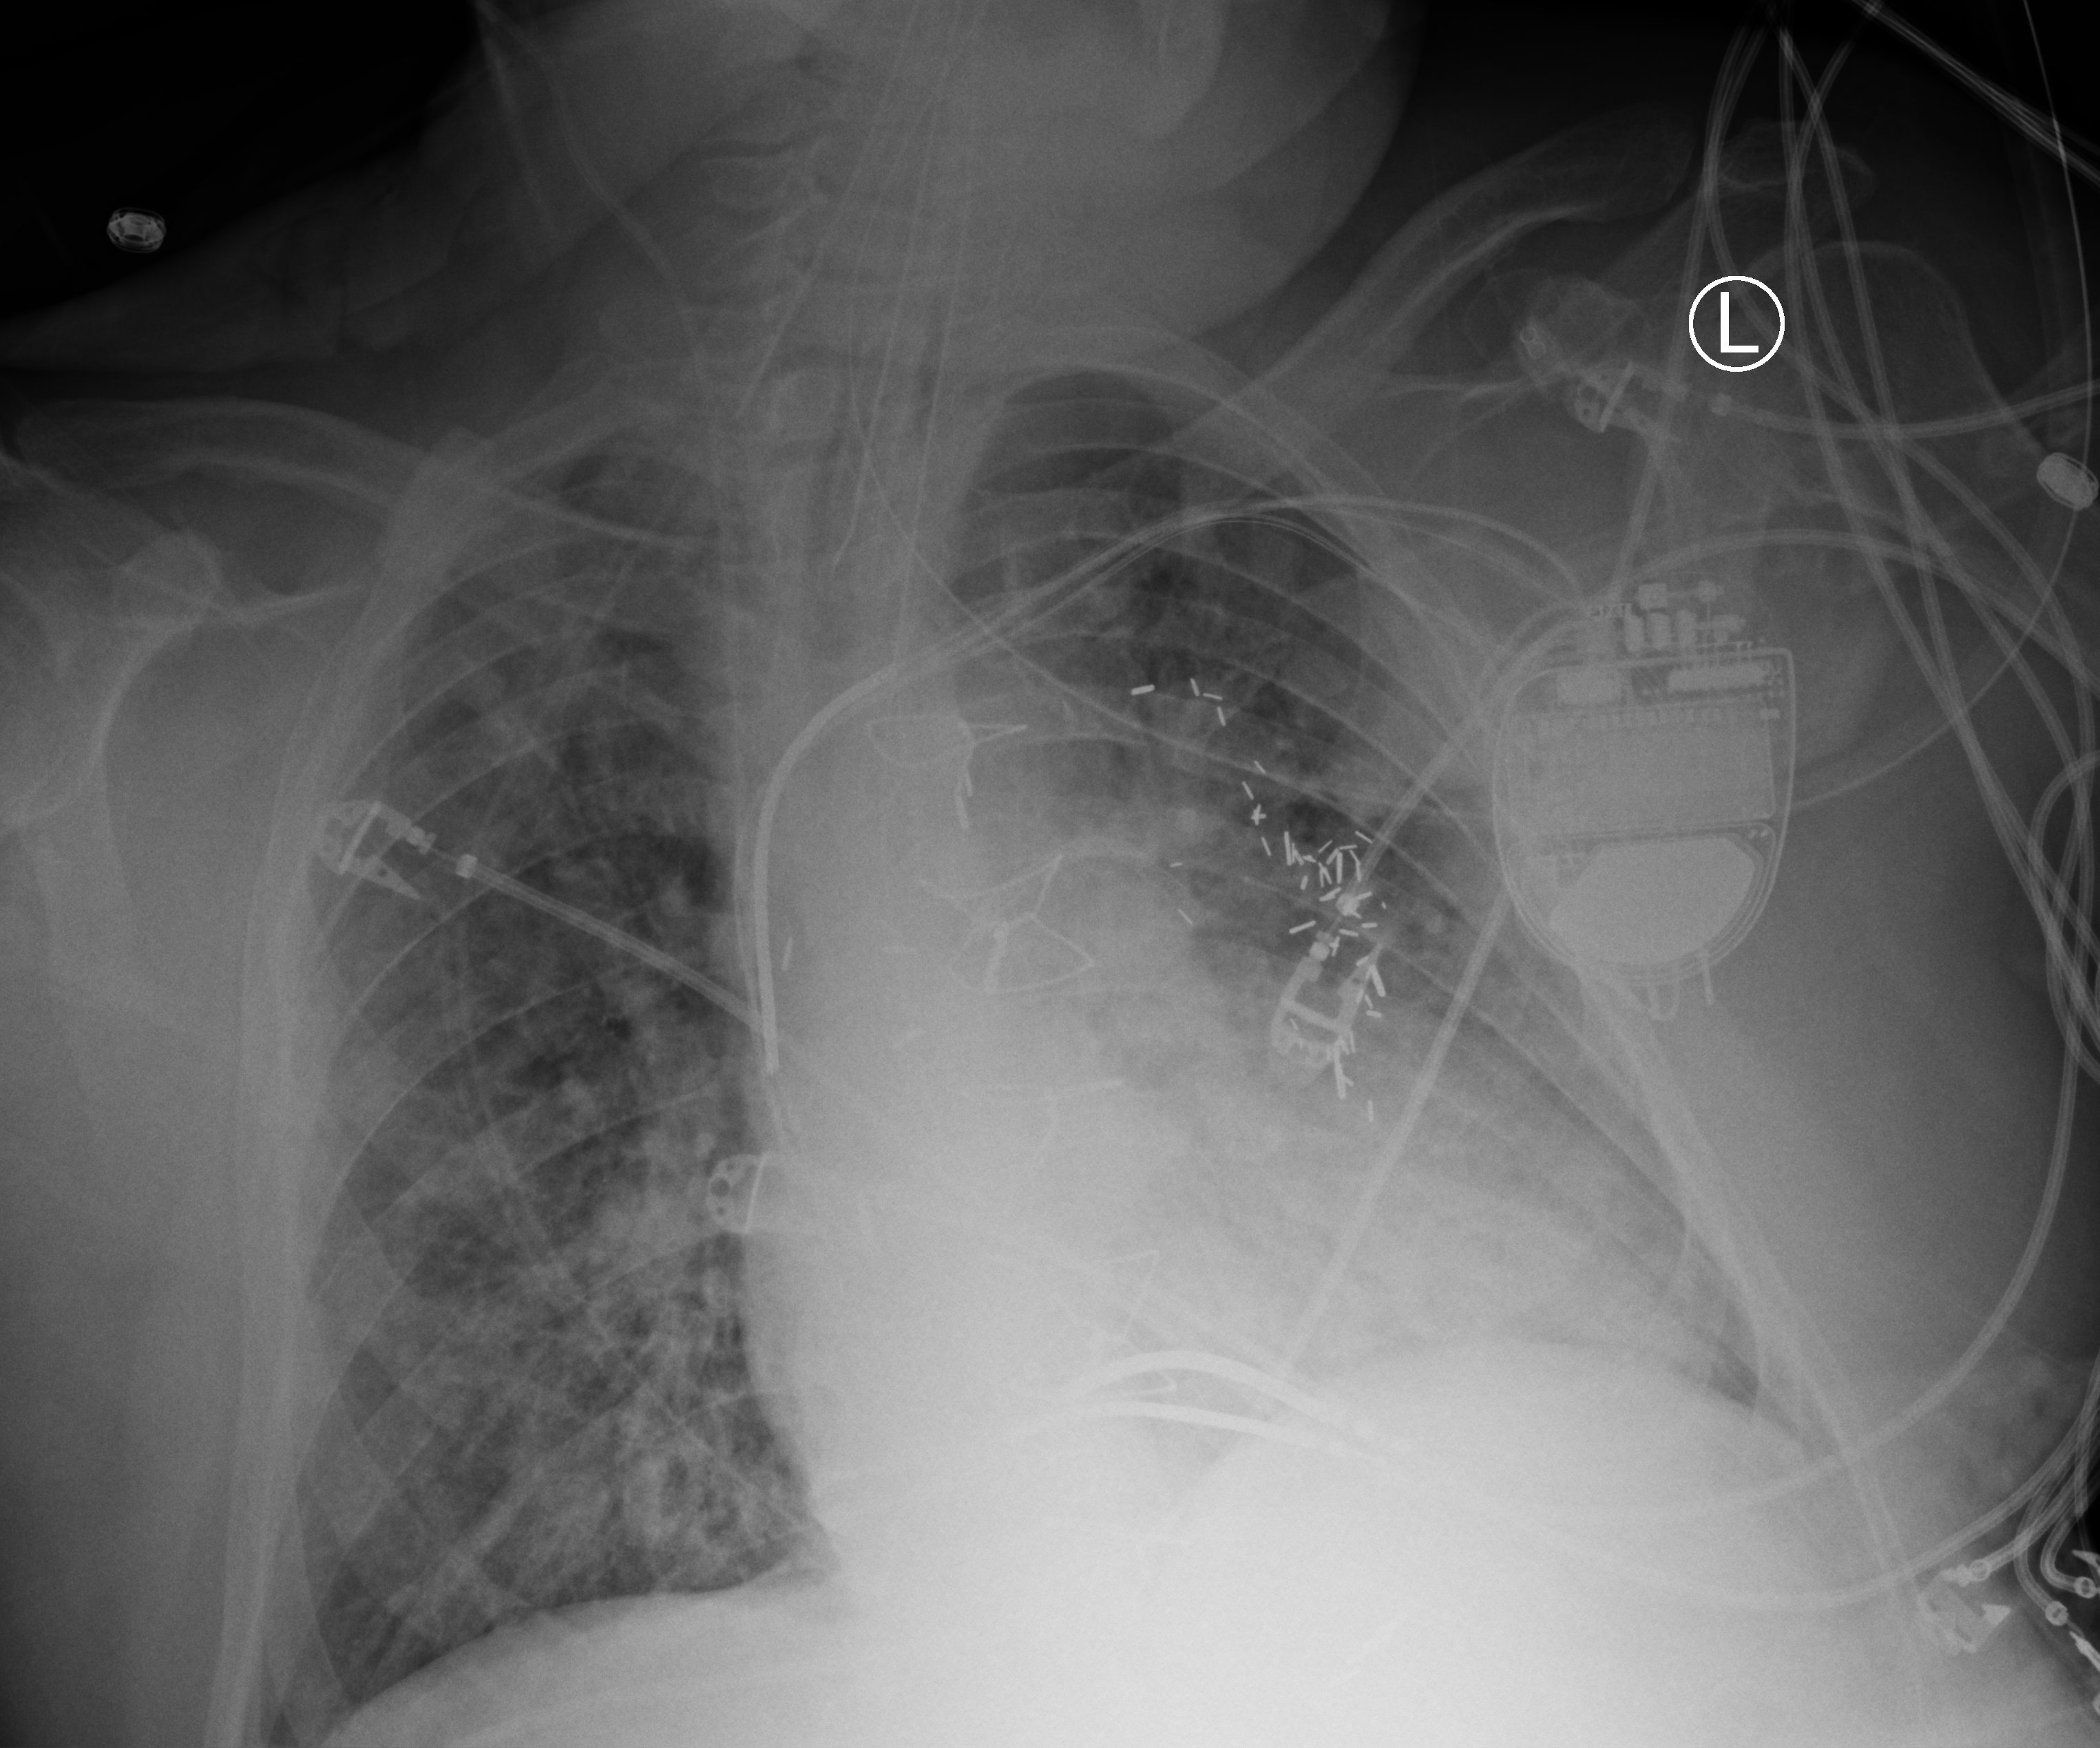
Chest X-ray (portable), anteroposterior (AP) projection. Male patient hospitalised with COVID-19, age 60–74 years.
From the hospital-stay record, not from the radiograph (when in the stay this image was taken is not recorded): mechanically ventilated during this hospital stay: yes.